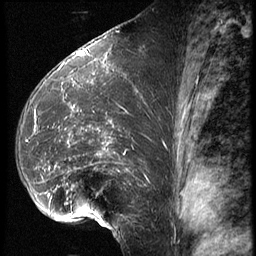
Breast MRI (dynamic contrast-enhanced), one sagittal slice; slice 35 of 62 in the series (ordered by position); 3 images stored at this slice position (order not interpretable as contrast timing); 1.5 T; TE 4.2 ms, TR 9 ms; 256 × 256 image matrix, field of view 180 × 180 mm. Female patient, age 39 years. From the clinical record (not read from this slice): setting: breast cancer imaged before/during neoadjuvant chemotherapy; receptor status: HER2-positive.
Outlined on this slice (semi-automatically segmented with operator editing):
- analysis volume of interest (the breast-tissue region the enhancement analysis was run in; not a lesion): bounding box [x1, y1, x2, y2] px = [17, 64, 161, 228]
- tumour enhancement mask (voxels above the 140 % enhancement threshold inside the analysis volume of interest): [33, 106, 129, 215]